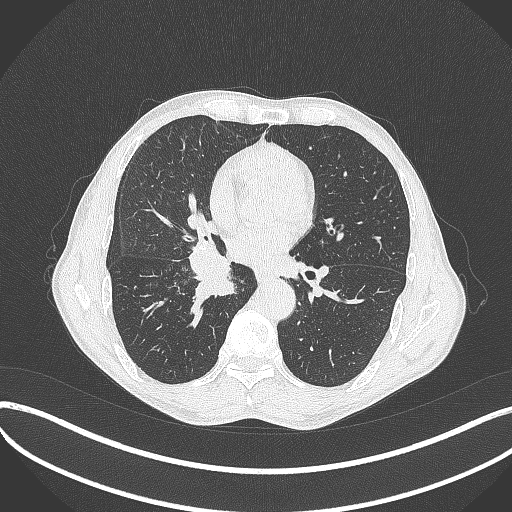
Chest CT, one axial slice. 120 kVp. Lung window (W 1500 / L -600 HU). 512 × 512 image matrix, field of view 400 × 400 mm. Male patient, age 65 years. Case-level facts recorded for this patient, not image findings: clinical TNM (as recorded): T2a N0 M0.
Annotated regions visible in this slice (bounding box drawn by a radiologist):
- lung tumour (recorded histology: squamous cell carcinoma): box from (x=181, y=237) to (x=240, y=303) px